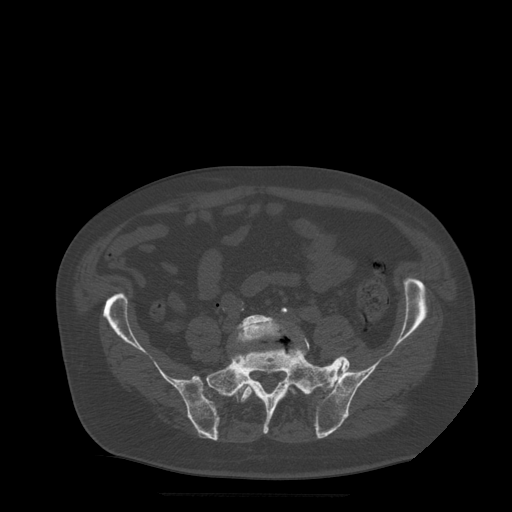
CT including the spine, one axial slice. Position 72 of 522 along the scan axis. Bone window (W 1800 / L 400 HU). 512 × 512 image matrix, field of view 420 × 420 mm. Patient age 72 years. Case-level facts recorded for this patient, not image findings: primary cancer: prostate.
Outlined on this slice (semi-automatically segmented with operator editing):
- L5 vertebra: bounding box <236,315,310,401> (left, top, right, bottom; pixels)